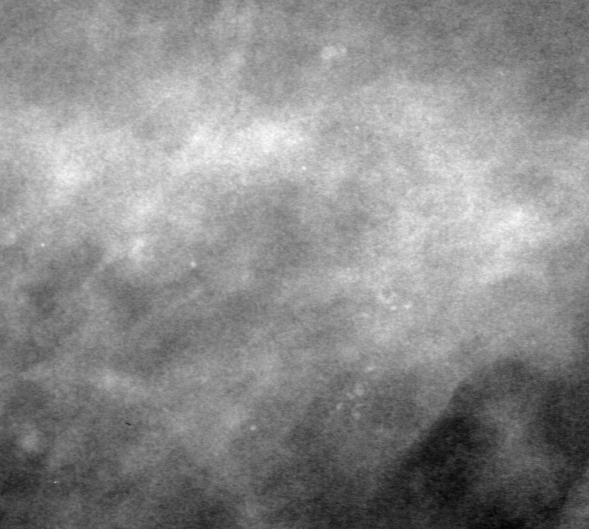
Region of interest cut from a scanned film mammogram (one marked finding), left breast, CC view, BI-RADS breast density category 2 (scale 1–4).
- Marked abnormality: calcifications, morphology amorphous, distribution clustered; BI-RADS assessment category 0 (incomplete: needs additional imaging); pathology (as recorded): malignant.